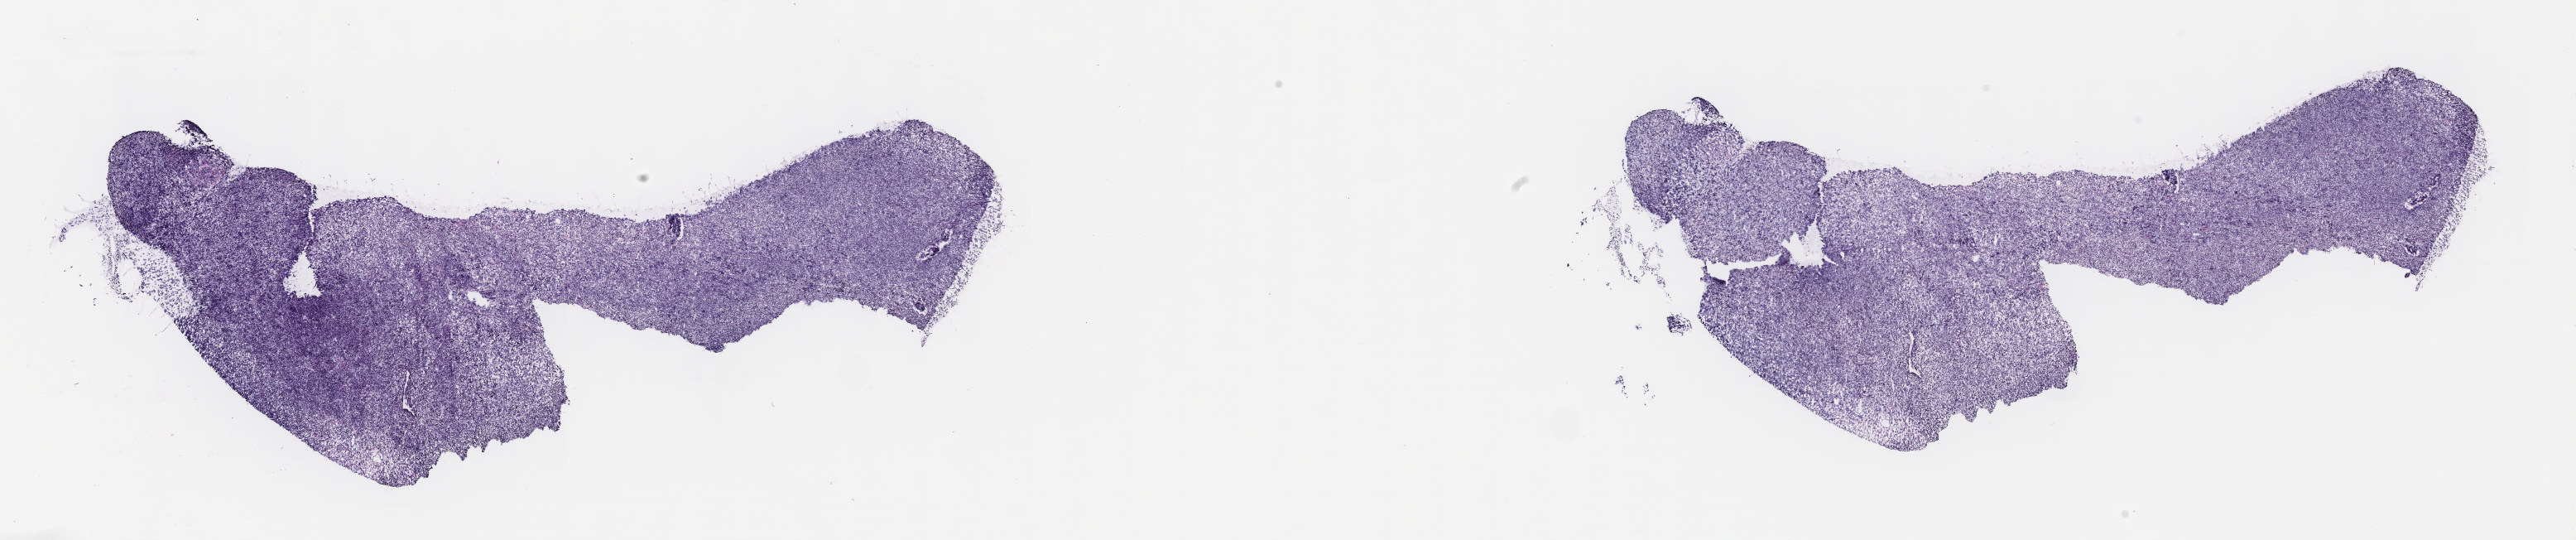
H&E whole-slide image — whole scanned area (about 25.2 x 5.3 mm) shown as a low-resolution overview, frozen section, specimen: primary tumor, site: cranium. Male, age 6 years at initial diagnosis. Slide review estimates, as recorded: tumor cells 90%, tumor nuclei 95%, stromal cells 5%, necrosis 5%, normal cells 0%. Infiltration values recorded for this section: lymphocyte infiltration 70%, monocyte infiltration 15%, neutrophil infiltration 0%.
• section: top of the tissue portion
• Ann Arbor stage (patient): Stage III
• diagnosis: Burkitt lymphoma, NOS